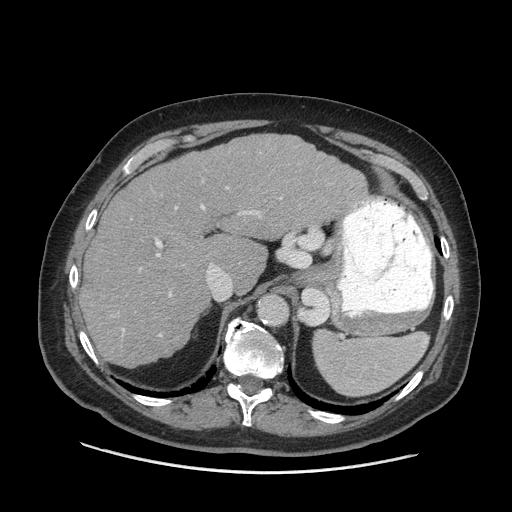
Contrast-enhanced abdominal CT (liver protocol), one axial slice. Reconstruction kernel STANDARD. Soft-tissue window (W 400 / L 40 HU). 512 × 512 image matrix. From the clinical record (not read from this slice): diagnosis: hepatocellular carcinoma (patient treated with transarterial chemoembolisation; whether this scan precedes or follows treatment is not stated here); TNM stage (as recorded): Stage-I; Child-Pugh class: A; tumour differentiation: well differentiated; tumour nodularity: uninodular.
Outlined on this slice (semi-automatic segmentation, software-assisted and operator-edited):
- liver parenchyma outside the tumour (the mass and vessels are separate outlines, so this box may not span the whole liver): box from (x=80, y=134) to (x=368, y=366) px
- liver vessels: (x=122, y=187)–(x=364, y=337)